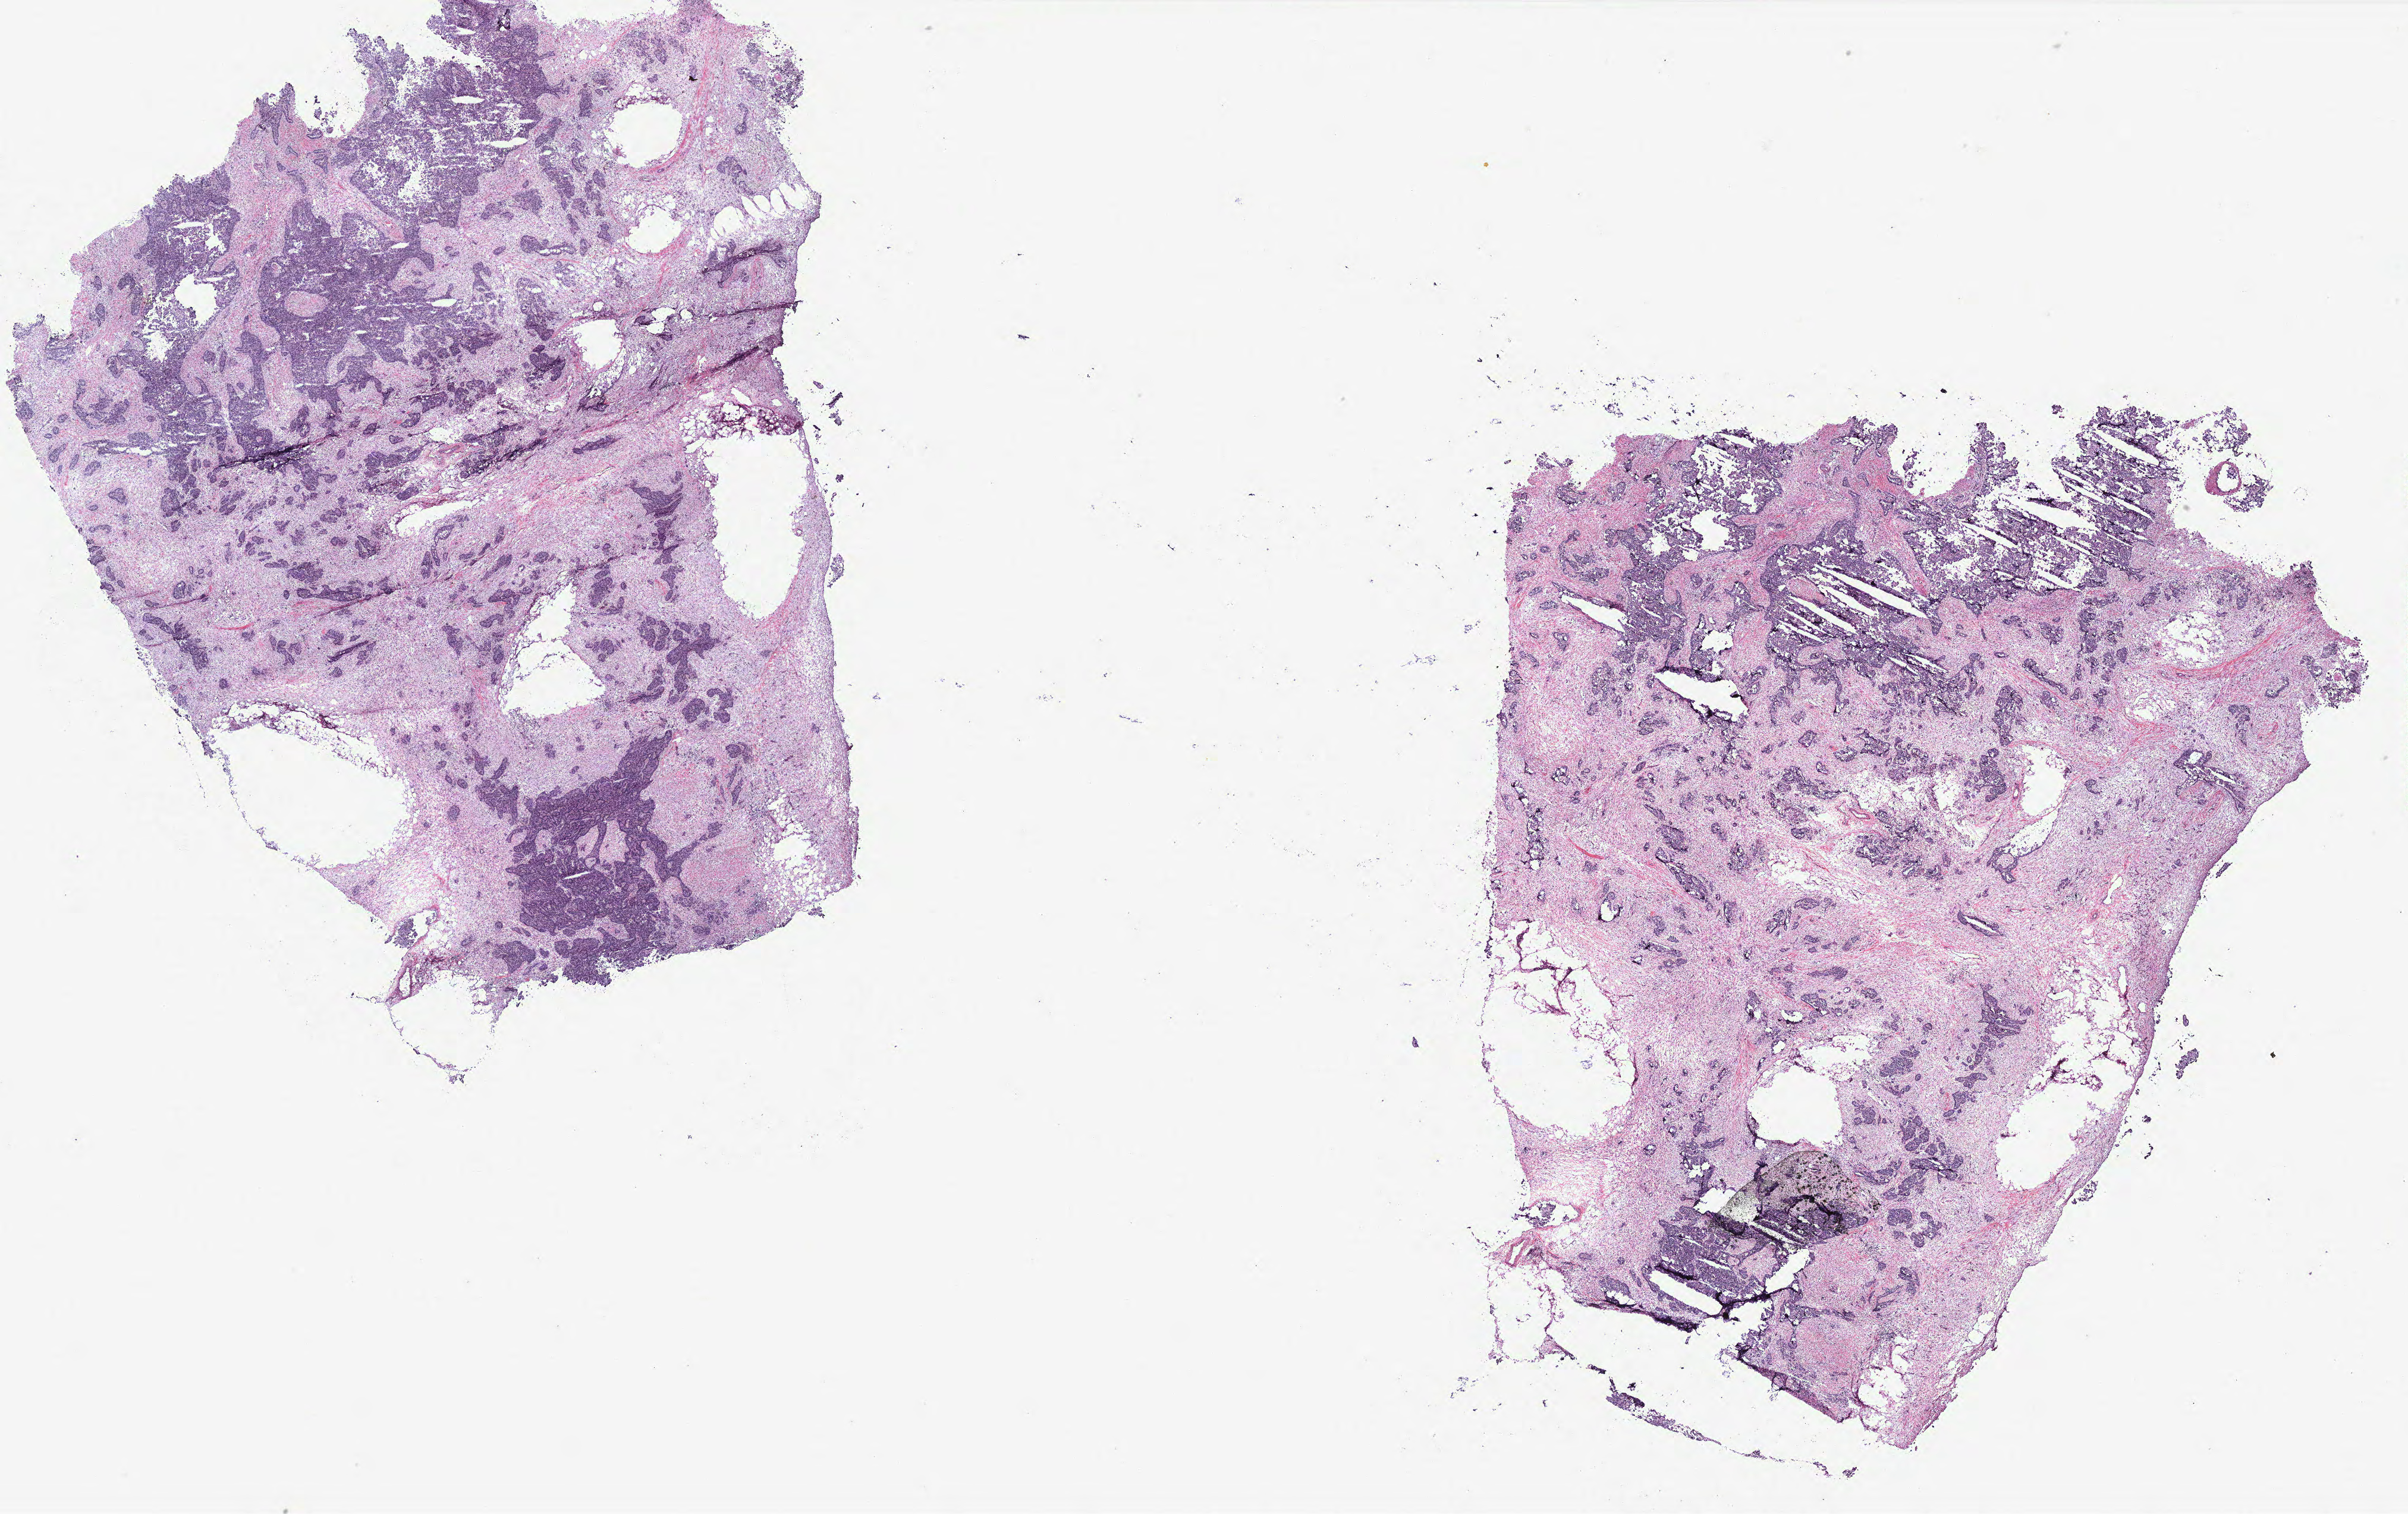
Whole-slide histology image, H&E, a low-resolution overview of the entire scanned area, about 32.4 x 20.4 mm. Tumour tissue sample, ovary. Female, 59 y/o.
Primary tumour site (as recorded): fallopian tube. Histologic diagnosis: Serous adenocarcinoma, NOS (fallopian tube).